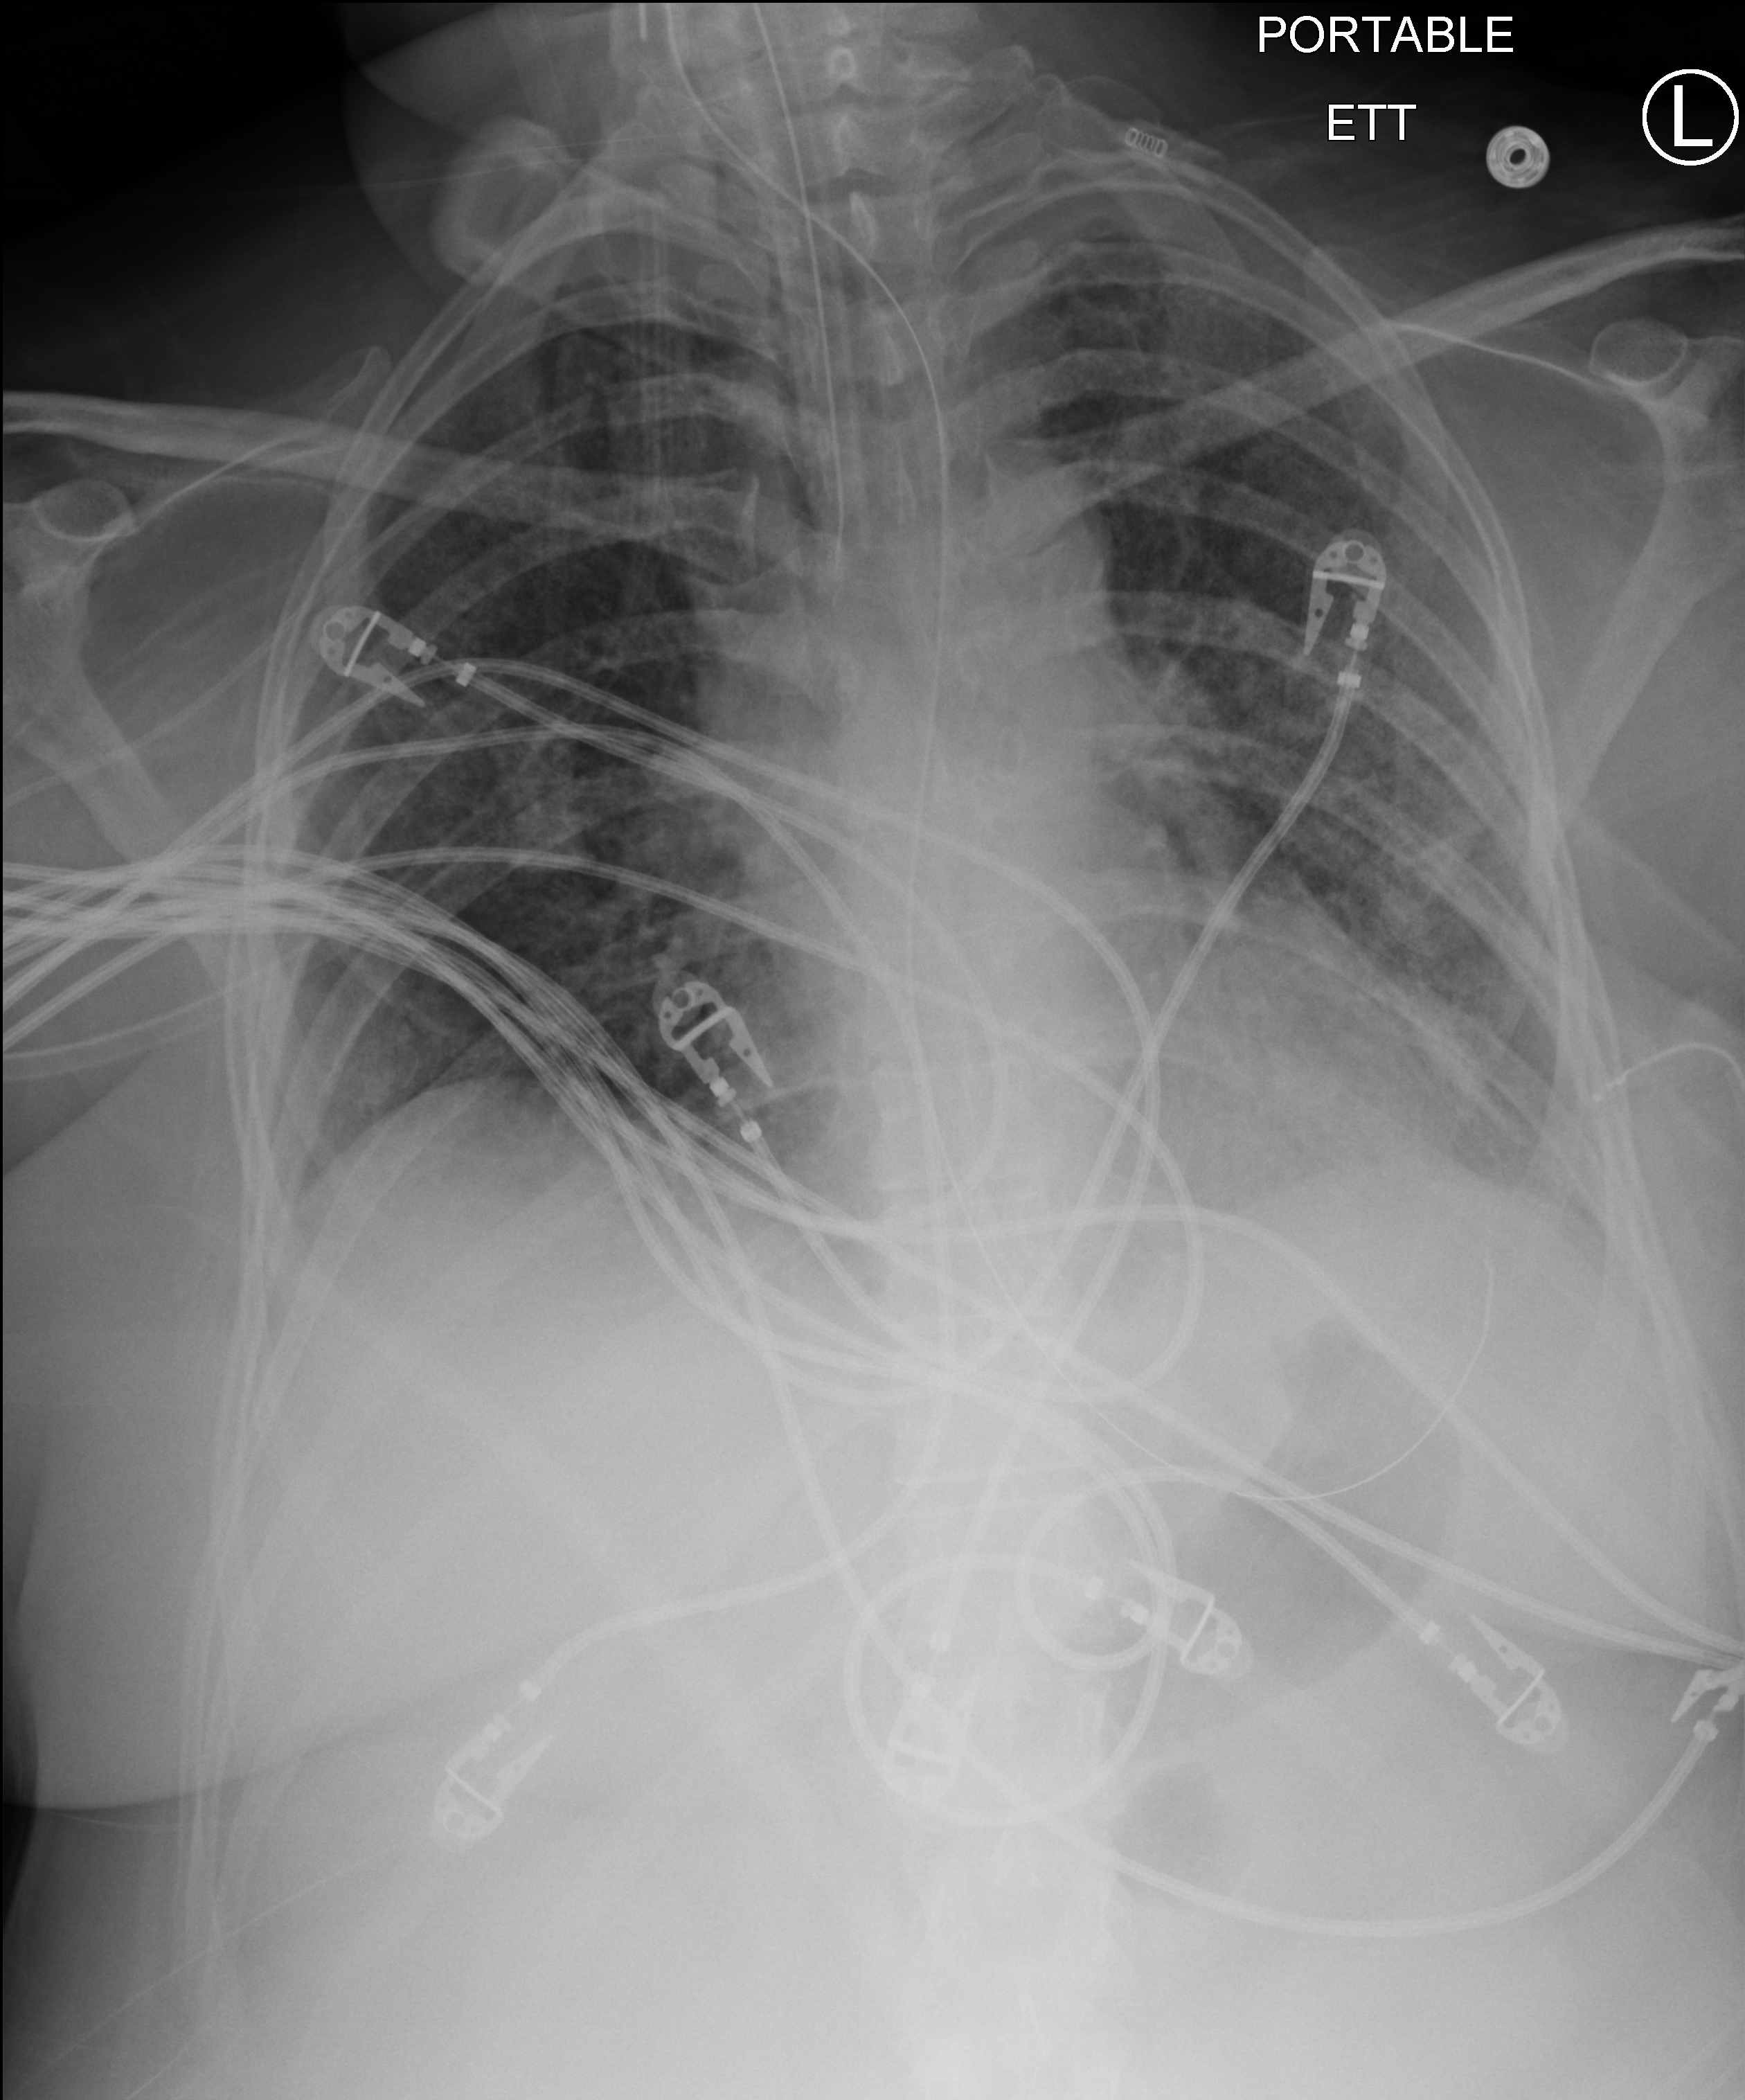
Bedside chest radiograph (computed radiography), anteroposterior (AP) projection. Female patient hospitalised with COVID-19, age 18–59 years.
Admission-level facts for this patient (not findings on this image; timing relative to this image not recorded):
- mechanically ventilated during this hospital stay: yes